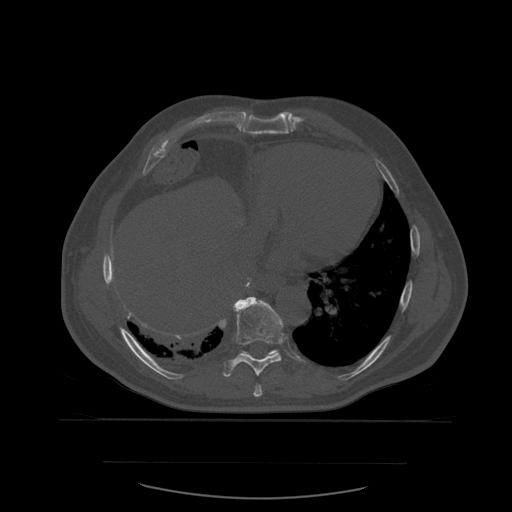
CT including the spine, one axial slice; position 337 of 590 along the scan axis; bone window (W 1800 / L 400 HU); 512 × 512 image matrix, field of view 479 × 479 mm. Patient age 71 years. Case-level facts recorded for this patient, not image findings: primary cancer: lung.
Outlined on this slice (semi-automatically segmented with operator editing):
- T10 vertebra: bounding box [x1, y1, x2, y2] px = [236, 298, 284, 354]
- T8 vertebra: [254, 384, 263, 397]
- T9 vertebra: [220, 297, 284, 377]